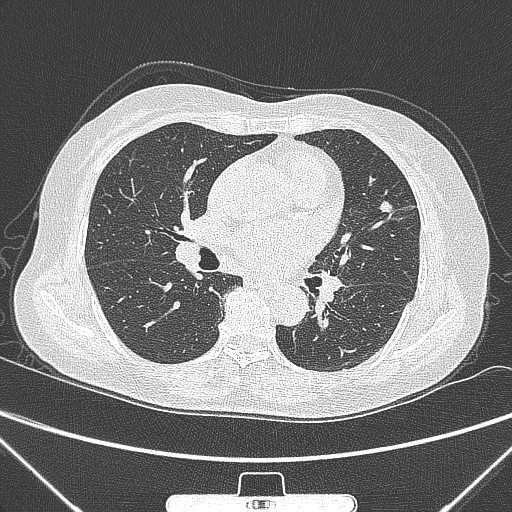
Chest CT, one axial slice; position 146 of 300 along the scan axis; lung window (W 1500 / L -600 HU); 1 mm slice thickness; 512 × 512 image matrix, field of view 350 × 350 mm. Female patient, age 70 years. From the clinical record (not read from this slice): clinical TNM (as recorded): T1b N0 M0; histopathological grade: G2.
Outlined on this slice (rectangle marked by the reading radiologist):
- lung tumour (recorded histology: adenocarcinoma): bounding box [x1, y1, x2, y2] px = [377, 199, 396, 219]